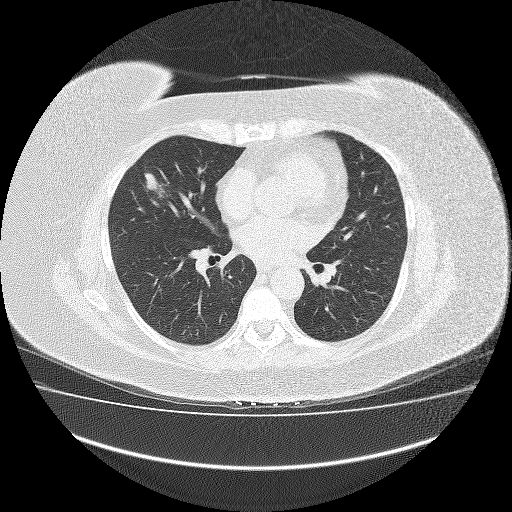
Axial slice from a low-dose chest CT screening exam; third screening round (two years after baseline); lung window (W 1500 / L -600 HU); 2 mm slice thickness; 512 × 512 image matrix, field of view 420 × 420 mm. Female participant, aged 64 years at enrolment. Former smoker at enrolment.
Expert-annotated lung lesion, bounding box <133,167,186,209> (left, top, right, bottom; pixels). Reader record for this screening exam (exam-level; its link to the box is not recorded): non-calcified nodule or mass ≥4 mm, right middle lobe, 23 × 13 mm, smooth margins, soft tissue attenuation, pre-existing on the prior screen: no. Official screen result: positive, other. Later outcome: lung cancer diagnosed 31 days after this screen — carcinoid tumor, NOS, right middle lobe, 3 mm at pathology.